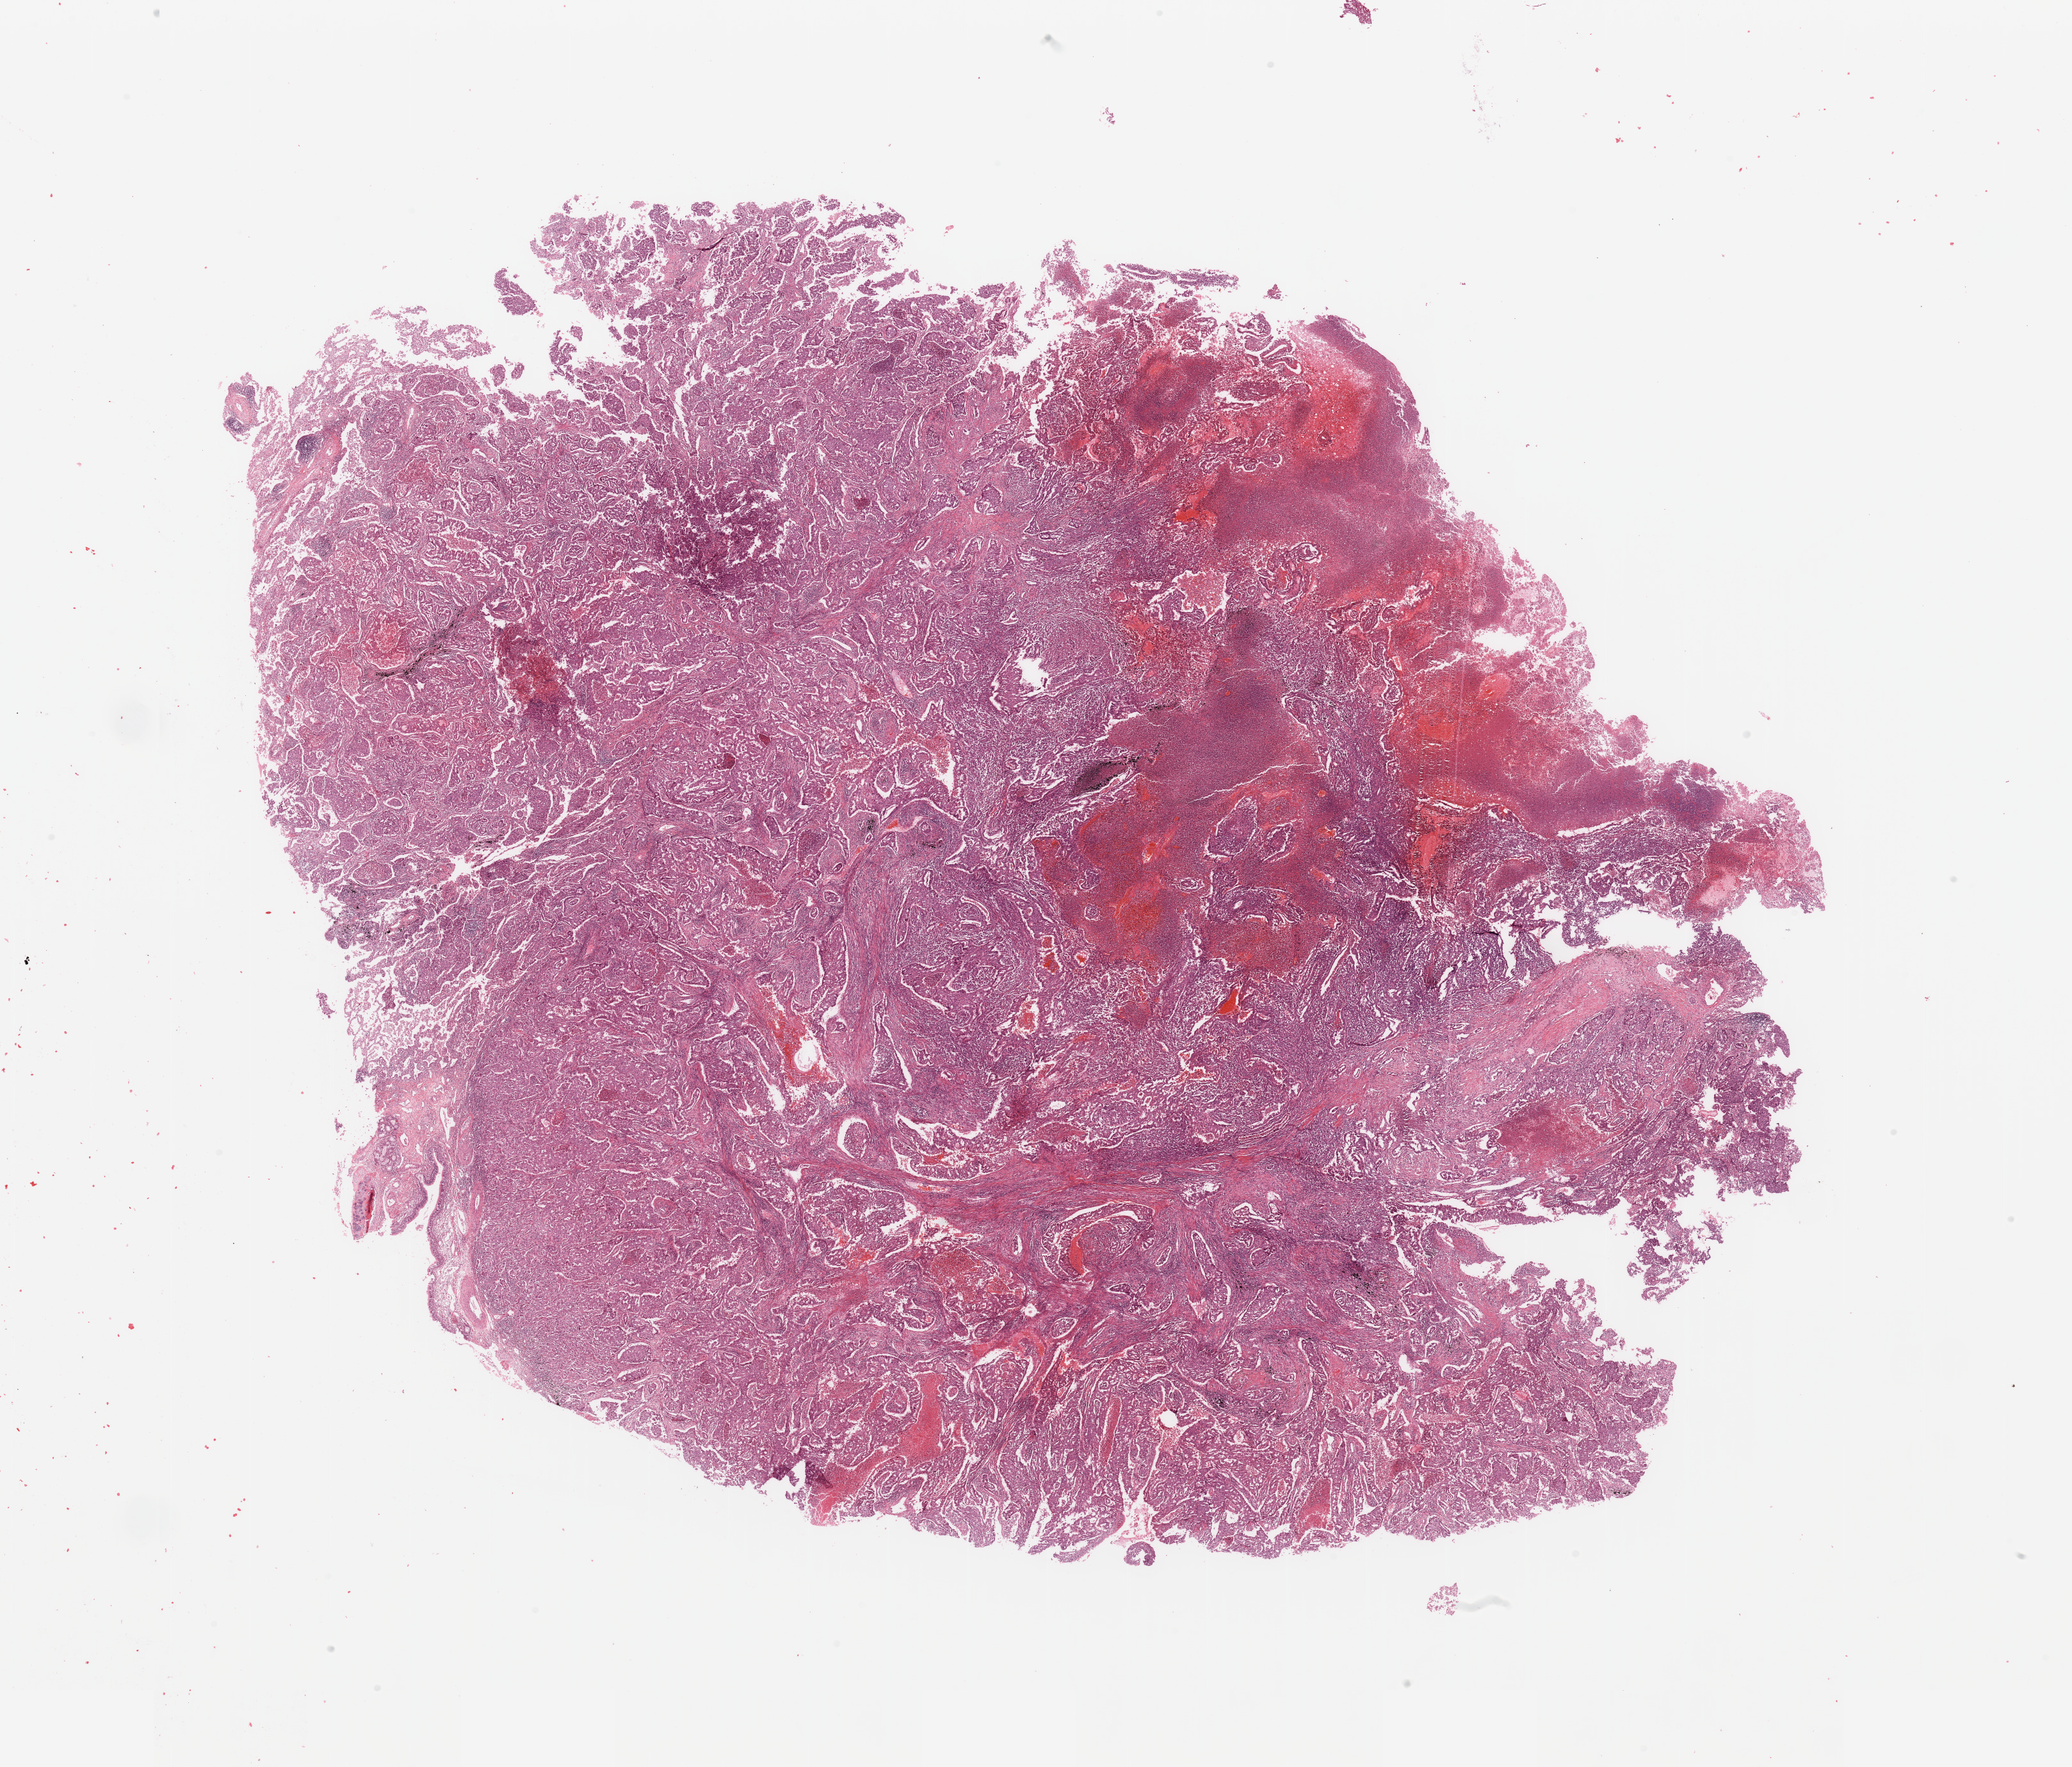
Whole-slide histology image, Hematoxylin and eosin (H&E) stained — whole scanned area (about 25.6 x 21.8 mm) shown as a low-resolution overview; lung, tumour tissue. Patient: male, age 63 years. Histologic grade: G2 (moderately differentiated).
• AJCC pathologic stage: IB
• histologic diagnosis: Adenocarcinoma, NOS